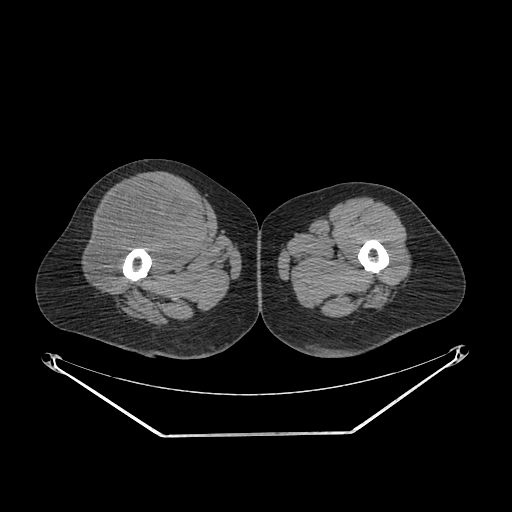
CT of an extremity soft-tissue mass (from a PET/CT study), one axial slice. Position 256 of 311 along the scan axis. Soft-tissue window (W 400 / L 40 HU). 3.75 mm slice thickness. 512 × 512 image matrix, field of view 500 × 500 mm. Female patient. From the clinical record (not read from this slice): histological type: pleiomorphic undifferentiated sarcoma; grade: high; site of the primary tumour: right quadricep.
Outlined on this slice (expert contour drawn on MRI and transferred to this co-registered scan by the dataset authors):
- tumour plus oedema (research contour): bounding box (x1, y1, x2, y2) in pixels: (91, 183, 199, 289)
- tumour (research contour): (91, 183, 199, 289)